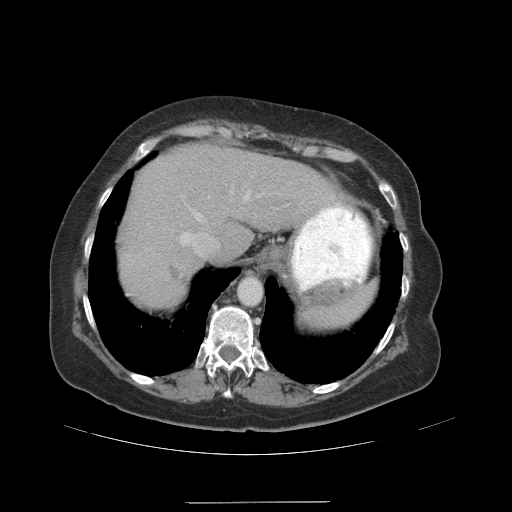
Contrast-enhanced abdominal CT (liver protocol), one axial slice. Position 79 of 99 along the scan axis. Soft-tissue window (W 400 / L 40 HU). 2.5 mm slice thickness. 512 × 512 image matrix. From the clinical record (not read from this slice): diagnosis: hepatocellular carcinoma (patient treated with transarterial chemoembolisation; whether this scan precedes or follows treatment is not stated here); TNM stage (as recorded): Stage-IVA; Child-Pugh class: A; tumour nodularity: multinodular.
Annotated regions visible in this slice (semi-automatically segmented with operator editing):
- abdominal aorta: box from (x=238, y=278) to (x=261, y=306) px
- liver parenchyma outside the tumour (the mass and vessels are separate outlines, so this box may not span the whole liver): (x=118, y=144)–(x=336, y=308)
- liver vessels: (x=180, y=194)–(x=259, y=248)